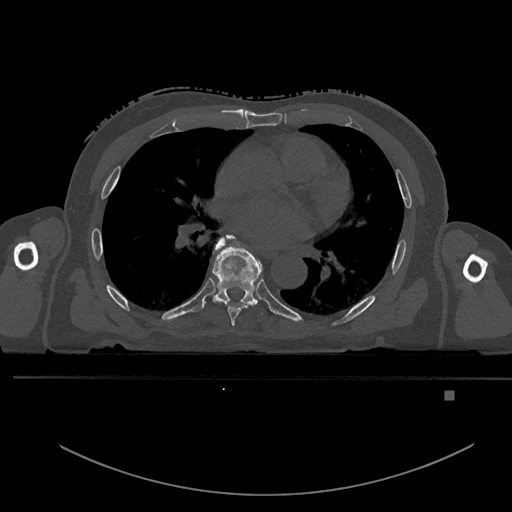
CT including the spine, one axial slice. Slice 278 of 969 in the series (ordered by position). Bone window (W 1800 / L 400 HU). 512 × 512 image matrix, field of view 456 × 456 mm. Male patient, age 82 years. From the clinical record (not read from this slice): primary cancer: prostate; vertebrae with lytic lesions (as recorded): T11, T9, T8, T2.
Structures marked on this image (semi-automatically segmented with operator editing):
- T6 vertebra: bounding box (x1, y1, x2, y2) in pixels: (215, 235, 250, 326)
- T7 vertebra: (211, 235, 262, 306)